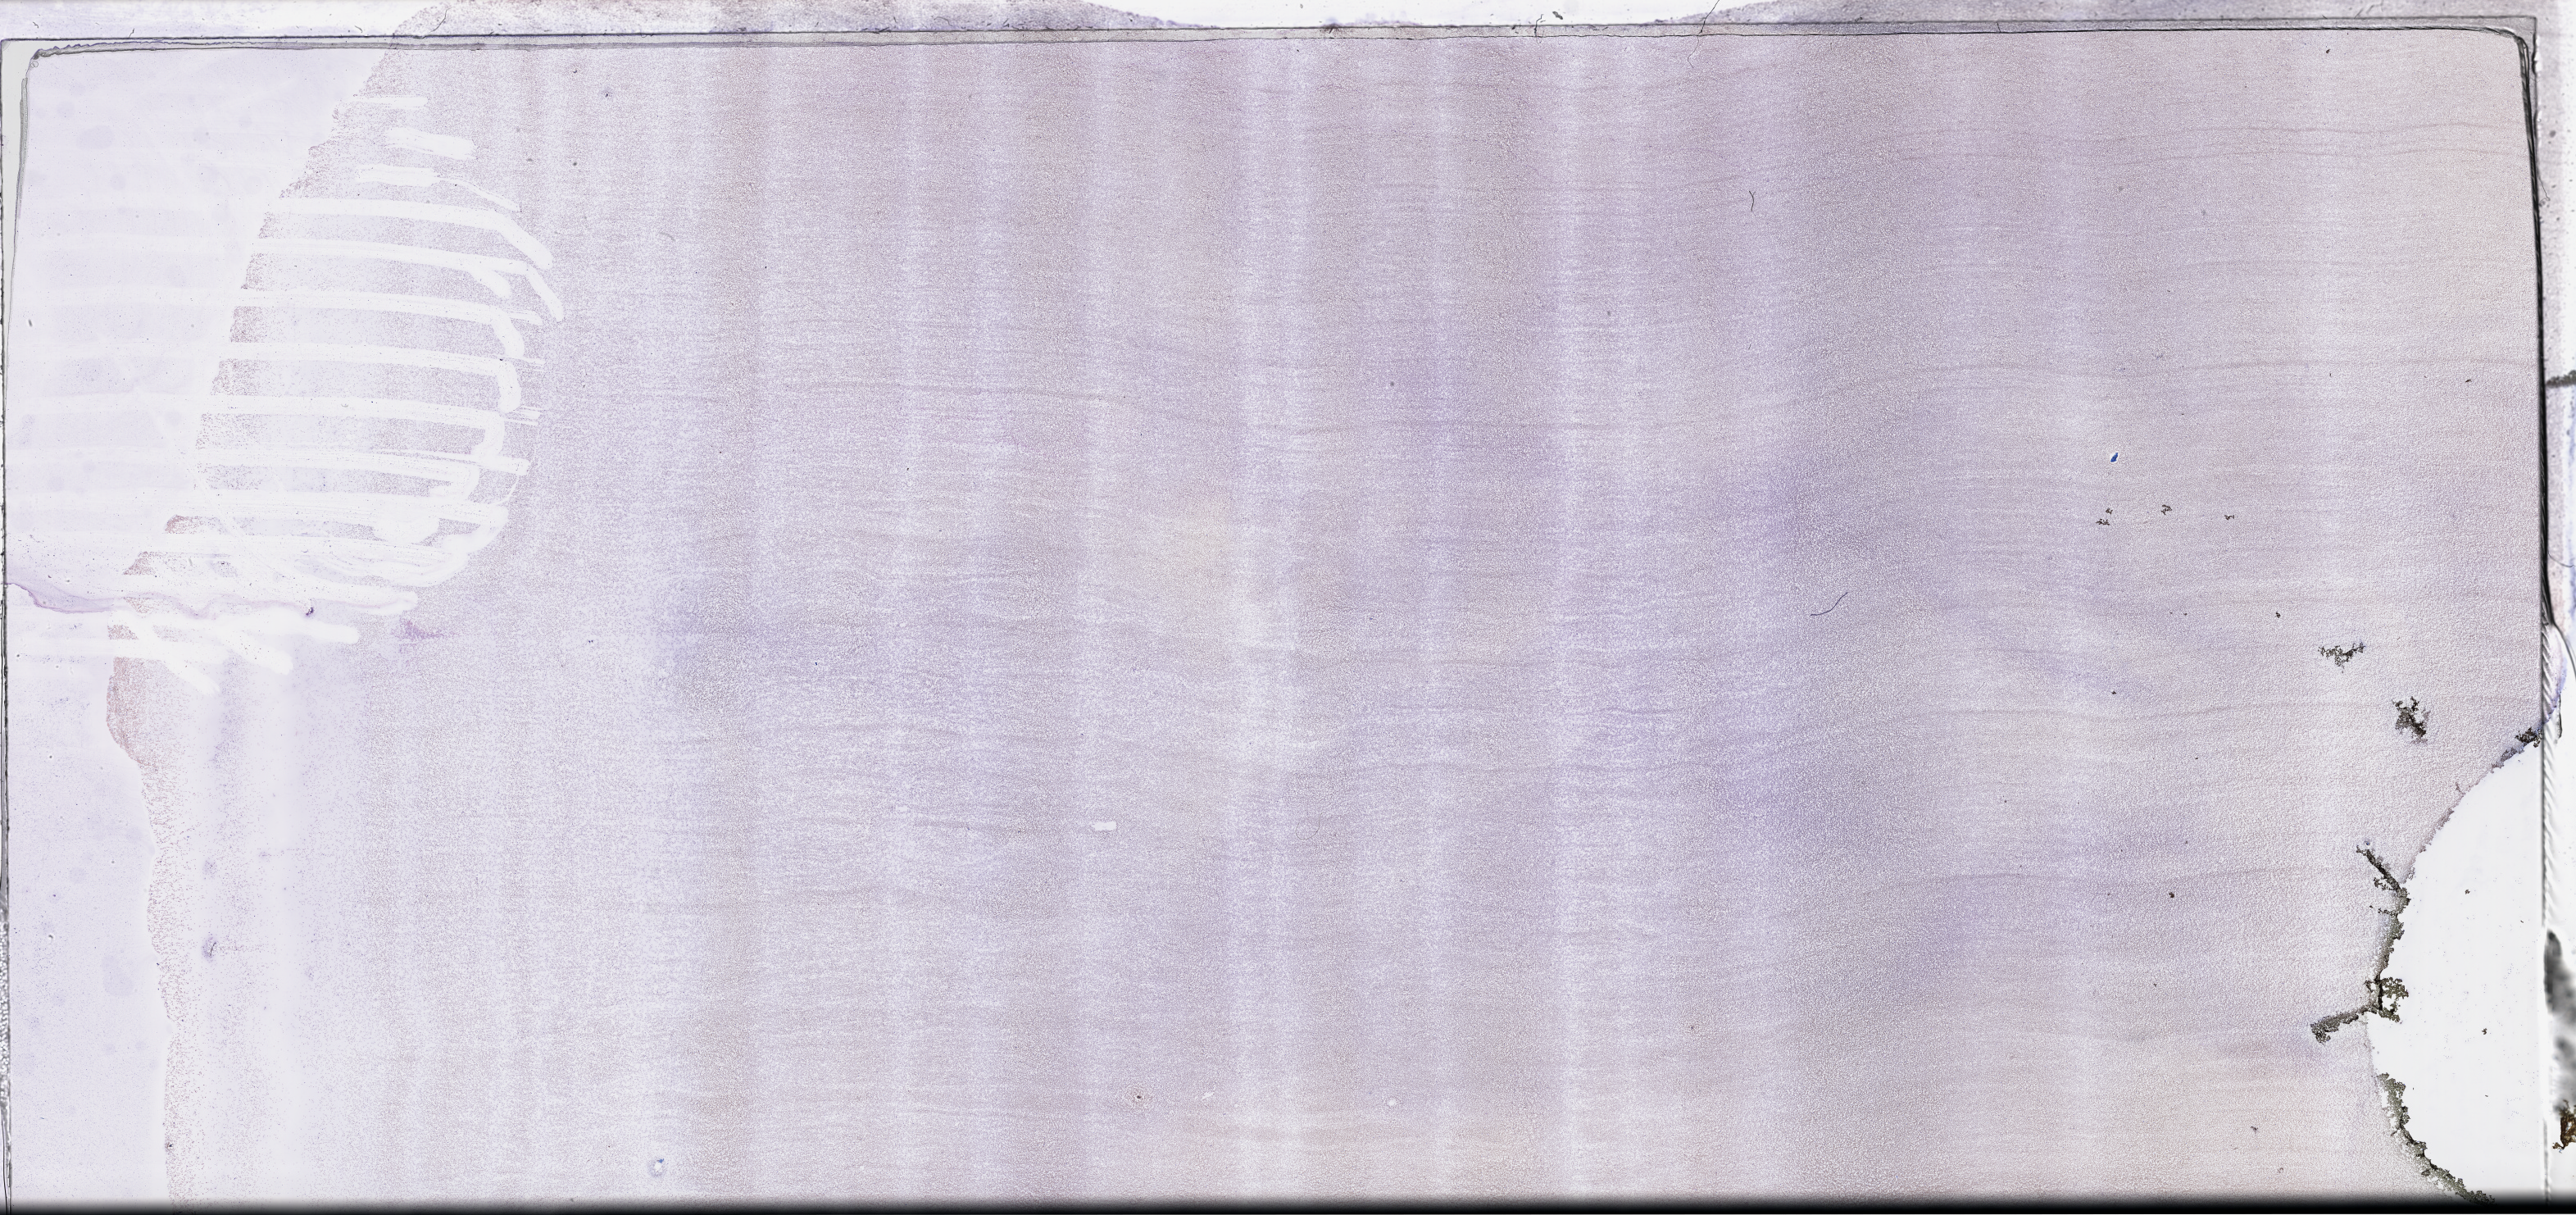
Wright–Giemsa-stained whole blood smear, whole-slide image — a low-resolution overview of the entire scanned area, about 50.8 x 23.9 mm, specimen time point: collected at baseline (before treatment). Patient sex: male.
Patient diagnosis: Plasma Cell Myeloma.